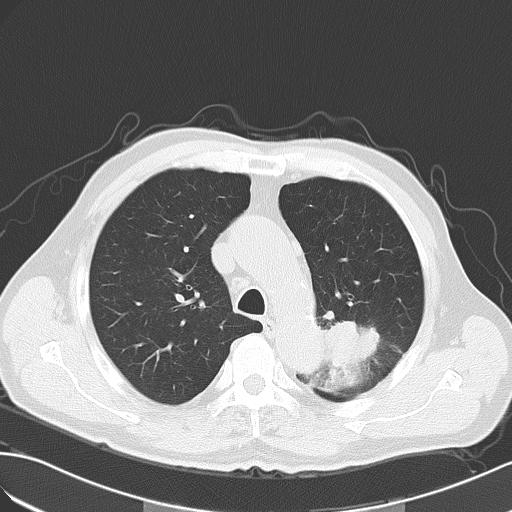
Chest CT, one axial slice. Position 41 of 55 along the scan axis. Reconstruction kernel B70f. Lung window (W 1500 / L -600 HU). 512 × 512 image matrix, field of view 353 × 353 mm. Male patient, age 63 years. From the clinical record (not read from this slice): clinical TNM (as recorded): T3 N3 M1a; histopathological grade: G3.
Structures marked on this image (bounding box drawn by a radiologist):
- lung tumour (recorded histology: large cell carcinoma): bounding box [x1, y1, x2, y2] px = [314, 310, 395, 389]